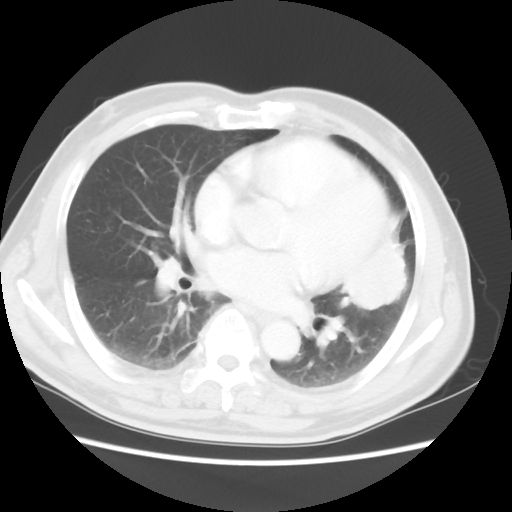
Chest CT, one axial slice; slice 23 of 50 in the series (ordered by position); reconstruction kernel STANDARD; 120 kVp; lung window (W 1500 / L -600 HU); 512 × 512 image matrix, field of view 360 × 360 mm. Male patient, age 69 years. From the clinical record (not read from this slice): clinical TNM (as recorded): T3 N1 M1a.
Outlined on this slice (bounding box drawn by a radiologist):
- lung tumour (recorded histology: squamous cell carcinoma): bounding box [x1, y1, x2, y2] px = [347, 230, 424, 319]